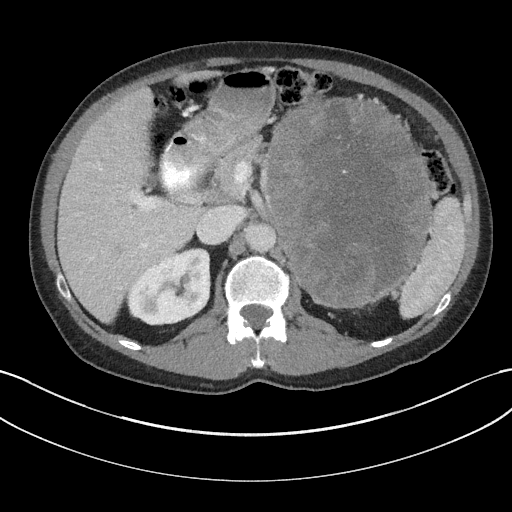
Contrast-enhanced abdominal CT, one axial slice; 100 kVp; intravenous contrast given; soft-tissue window (W 400 / L 40 HU); 3 mm slice thickness; 512 × 512 image matrix, field of view 384 × 384 mm. Male patient, age 58 years. From the clinical record (not read from this slice): diagnosis: adrenocortical carcinoma; tumour side: left adrenal; tumour size at pathology: 22 cm; Ki-67 index: 26 %; stage (as recorded): 2.
Outlined on this slice (semi-automatic segmentation, software-assisted and operator-edited):
- mass: bounding box <266,102,432,306> (left, top, right, bottom; pixels)